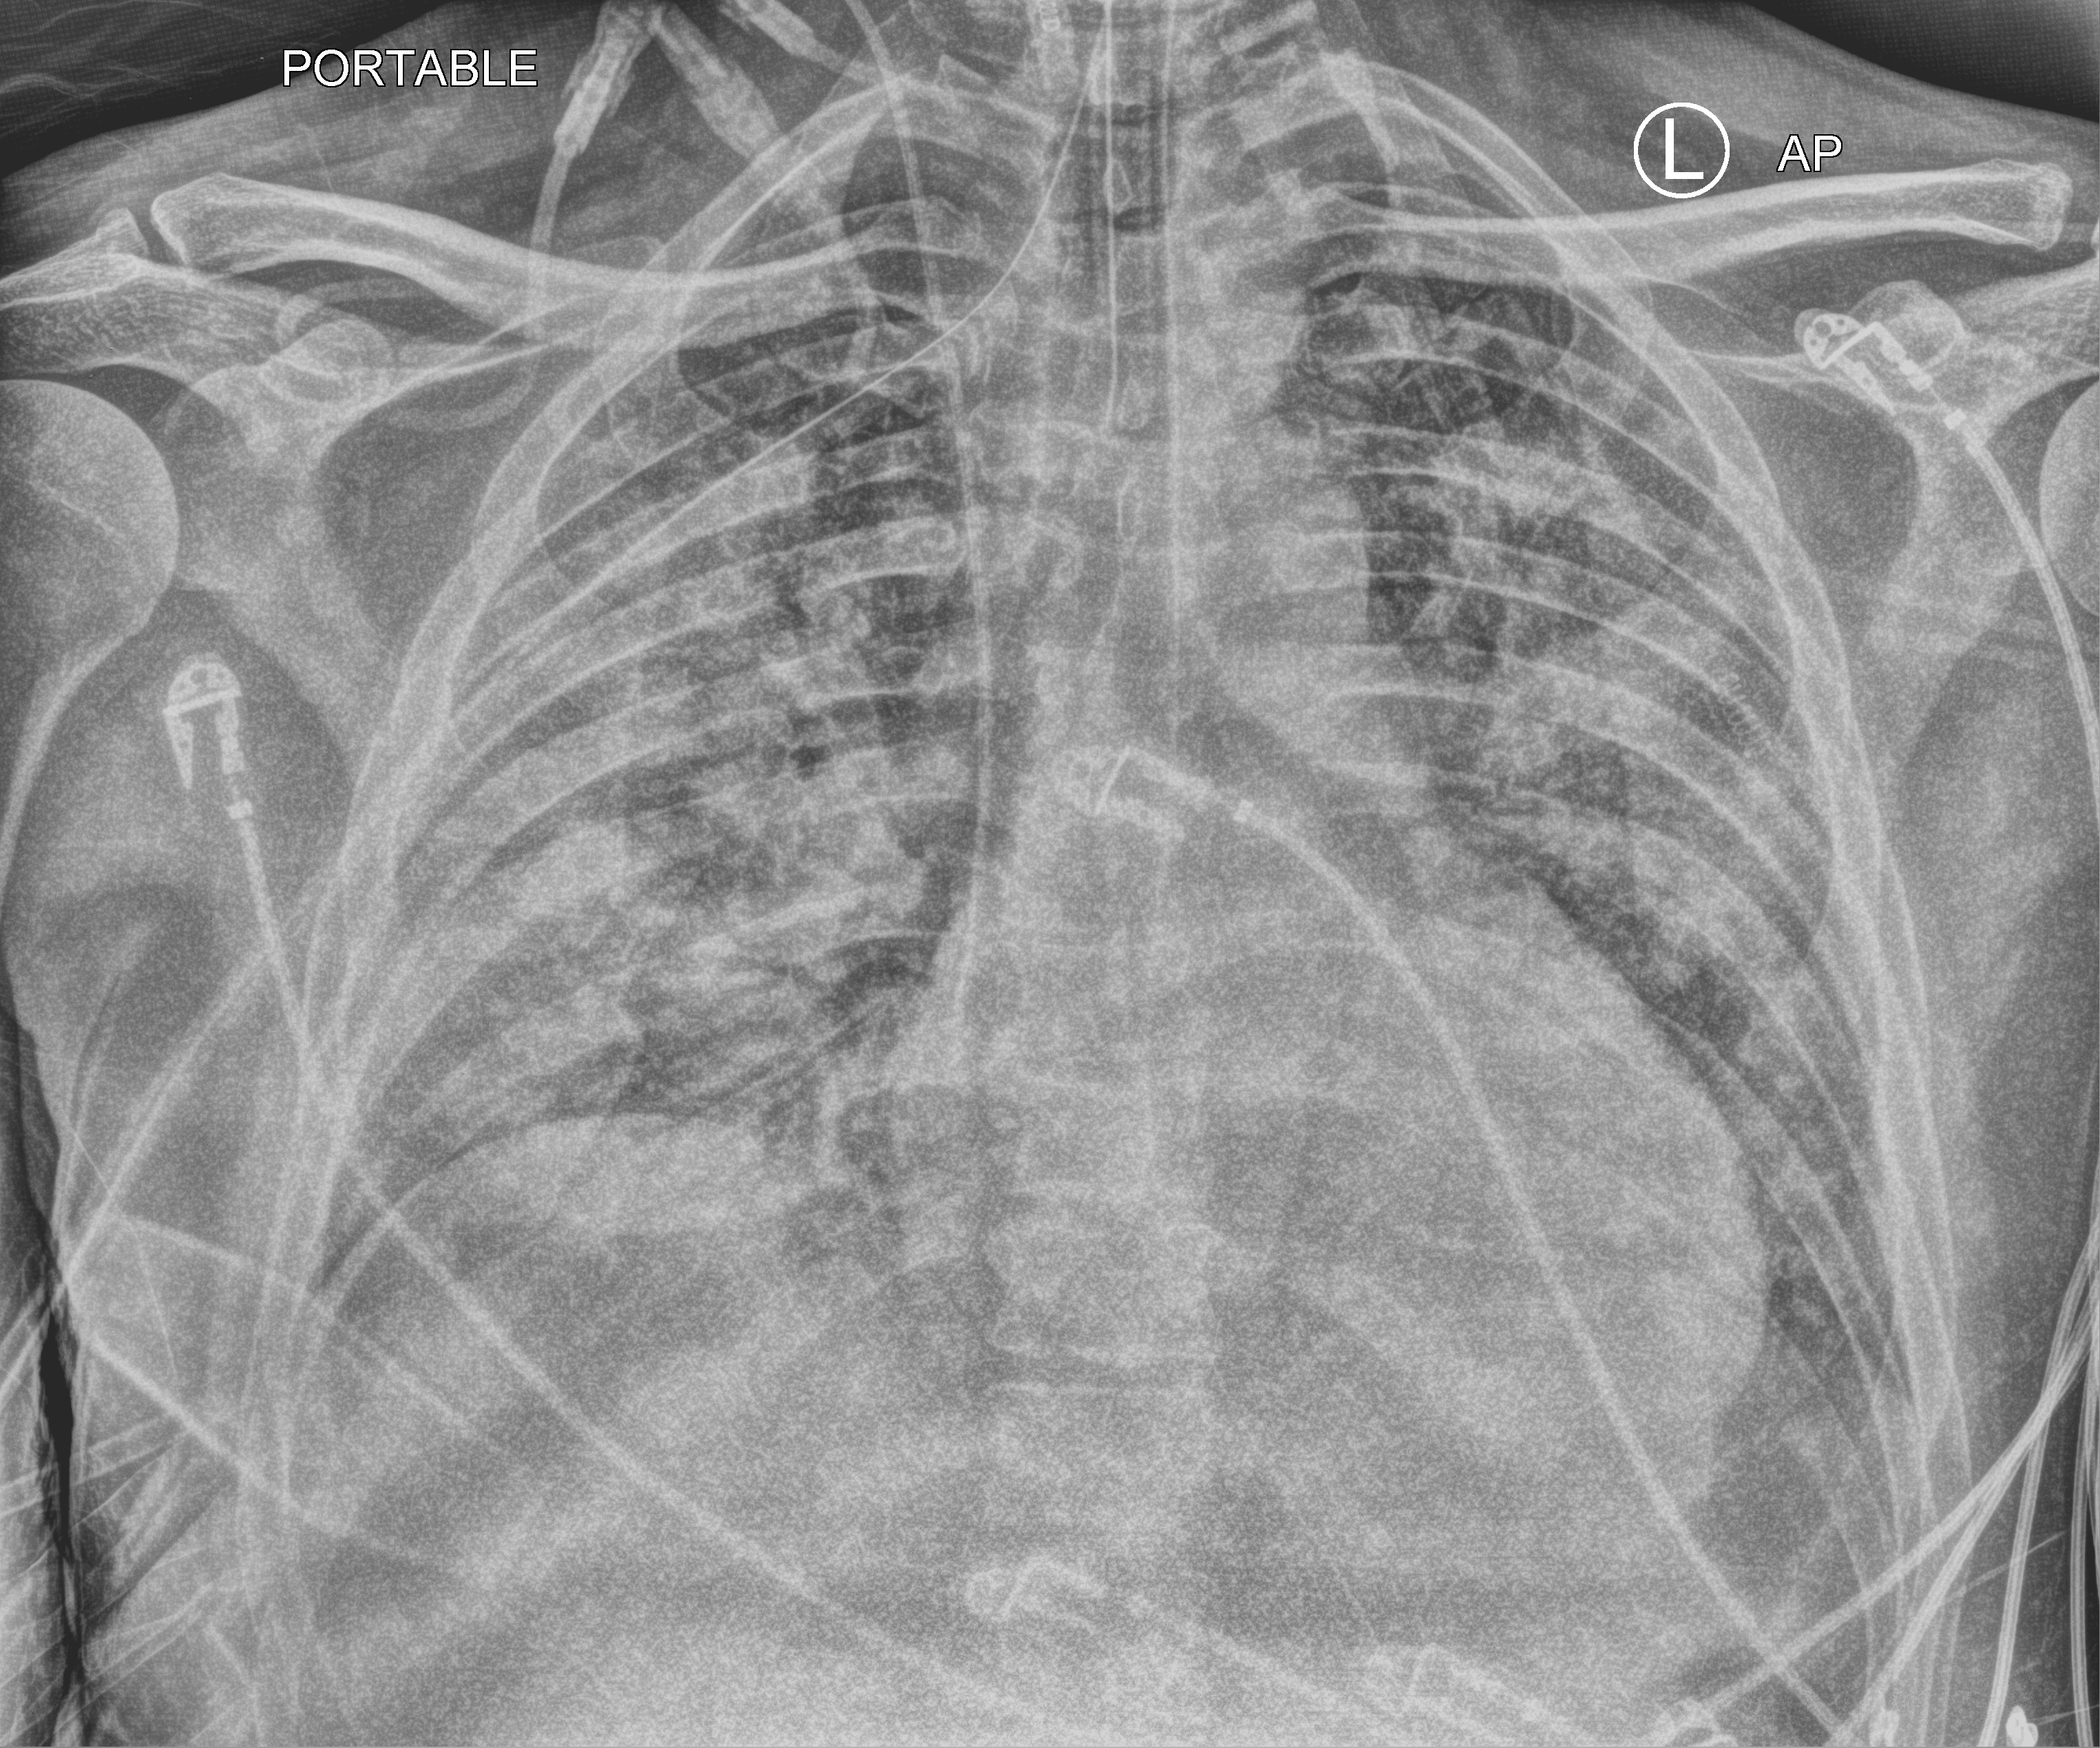
Portable chest radiograph; anteroposterior (AP) projection. Patient hospitalised with COVID-19; male, aged 18–59 years.
Hospital-stay facts (about this admission, not read from this image; timing relative to this image not recorded): admitted to intensive care during this hospital stay: yes.